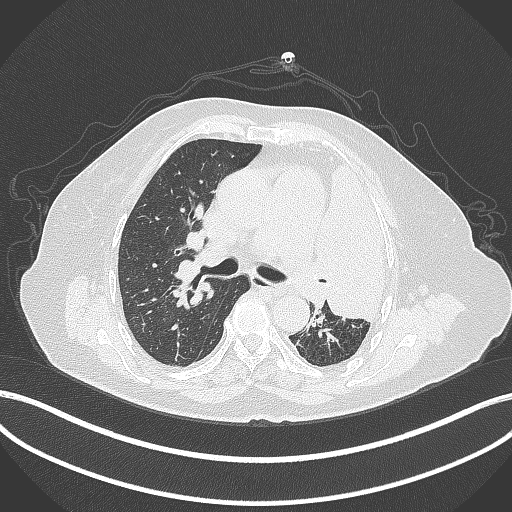
Chest CT, one axial slice; position 241 of 399 along the scan axis; reconstruction kernel B70f; 120 kVp; lung window (W 1500 / L -600 HU); 1 mm slice thickness; 512 × 512 image matrix, field of view 400 × 400 mm. Female patient, age 75 years. Case-level facts recorded for this patient, not image findings: clinical TNM (as recorded): T3 N3 M1.
Structures marked on this image (rectangle marked by the reading radiologist):
- lung tumour (recorded histology: adenocarcinoma): bounding box <305,156,398,328> (left, top, right, bottom; pixels)